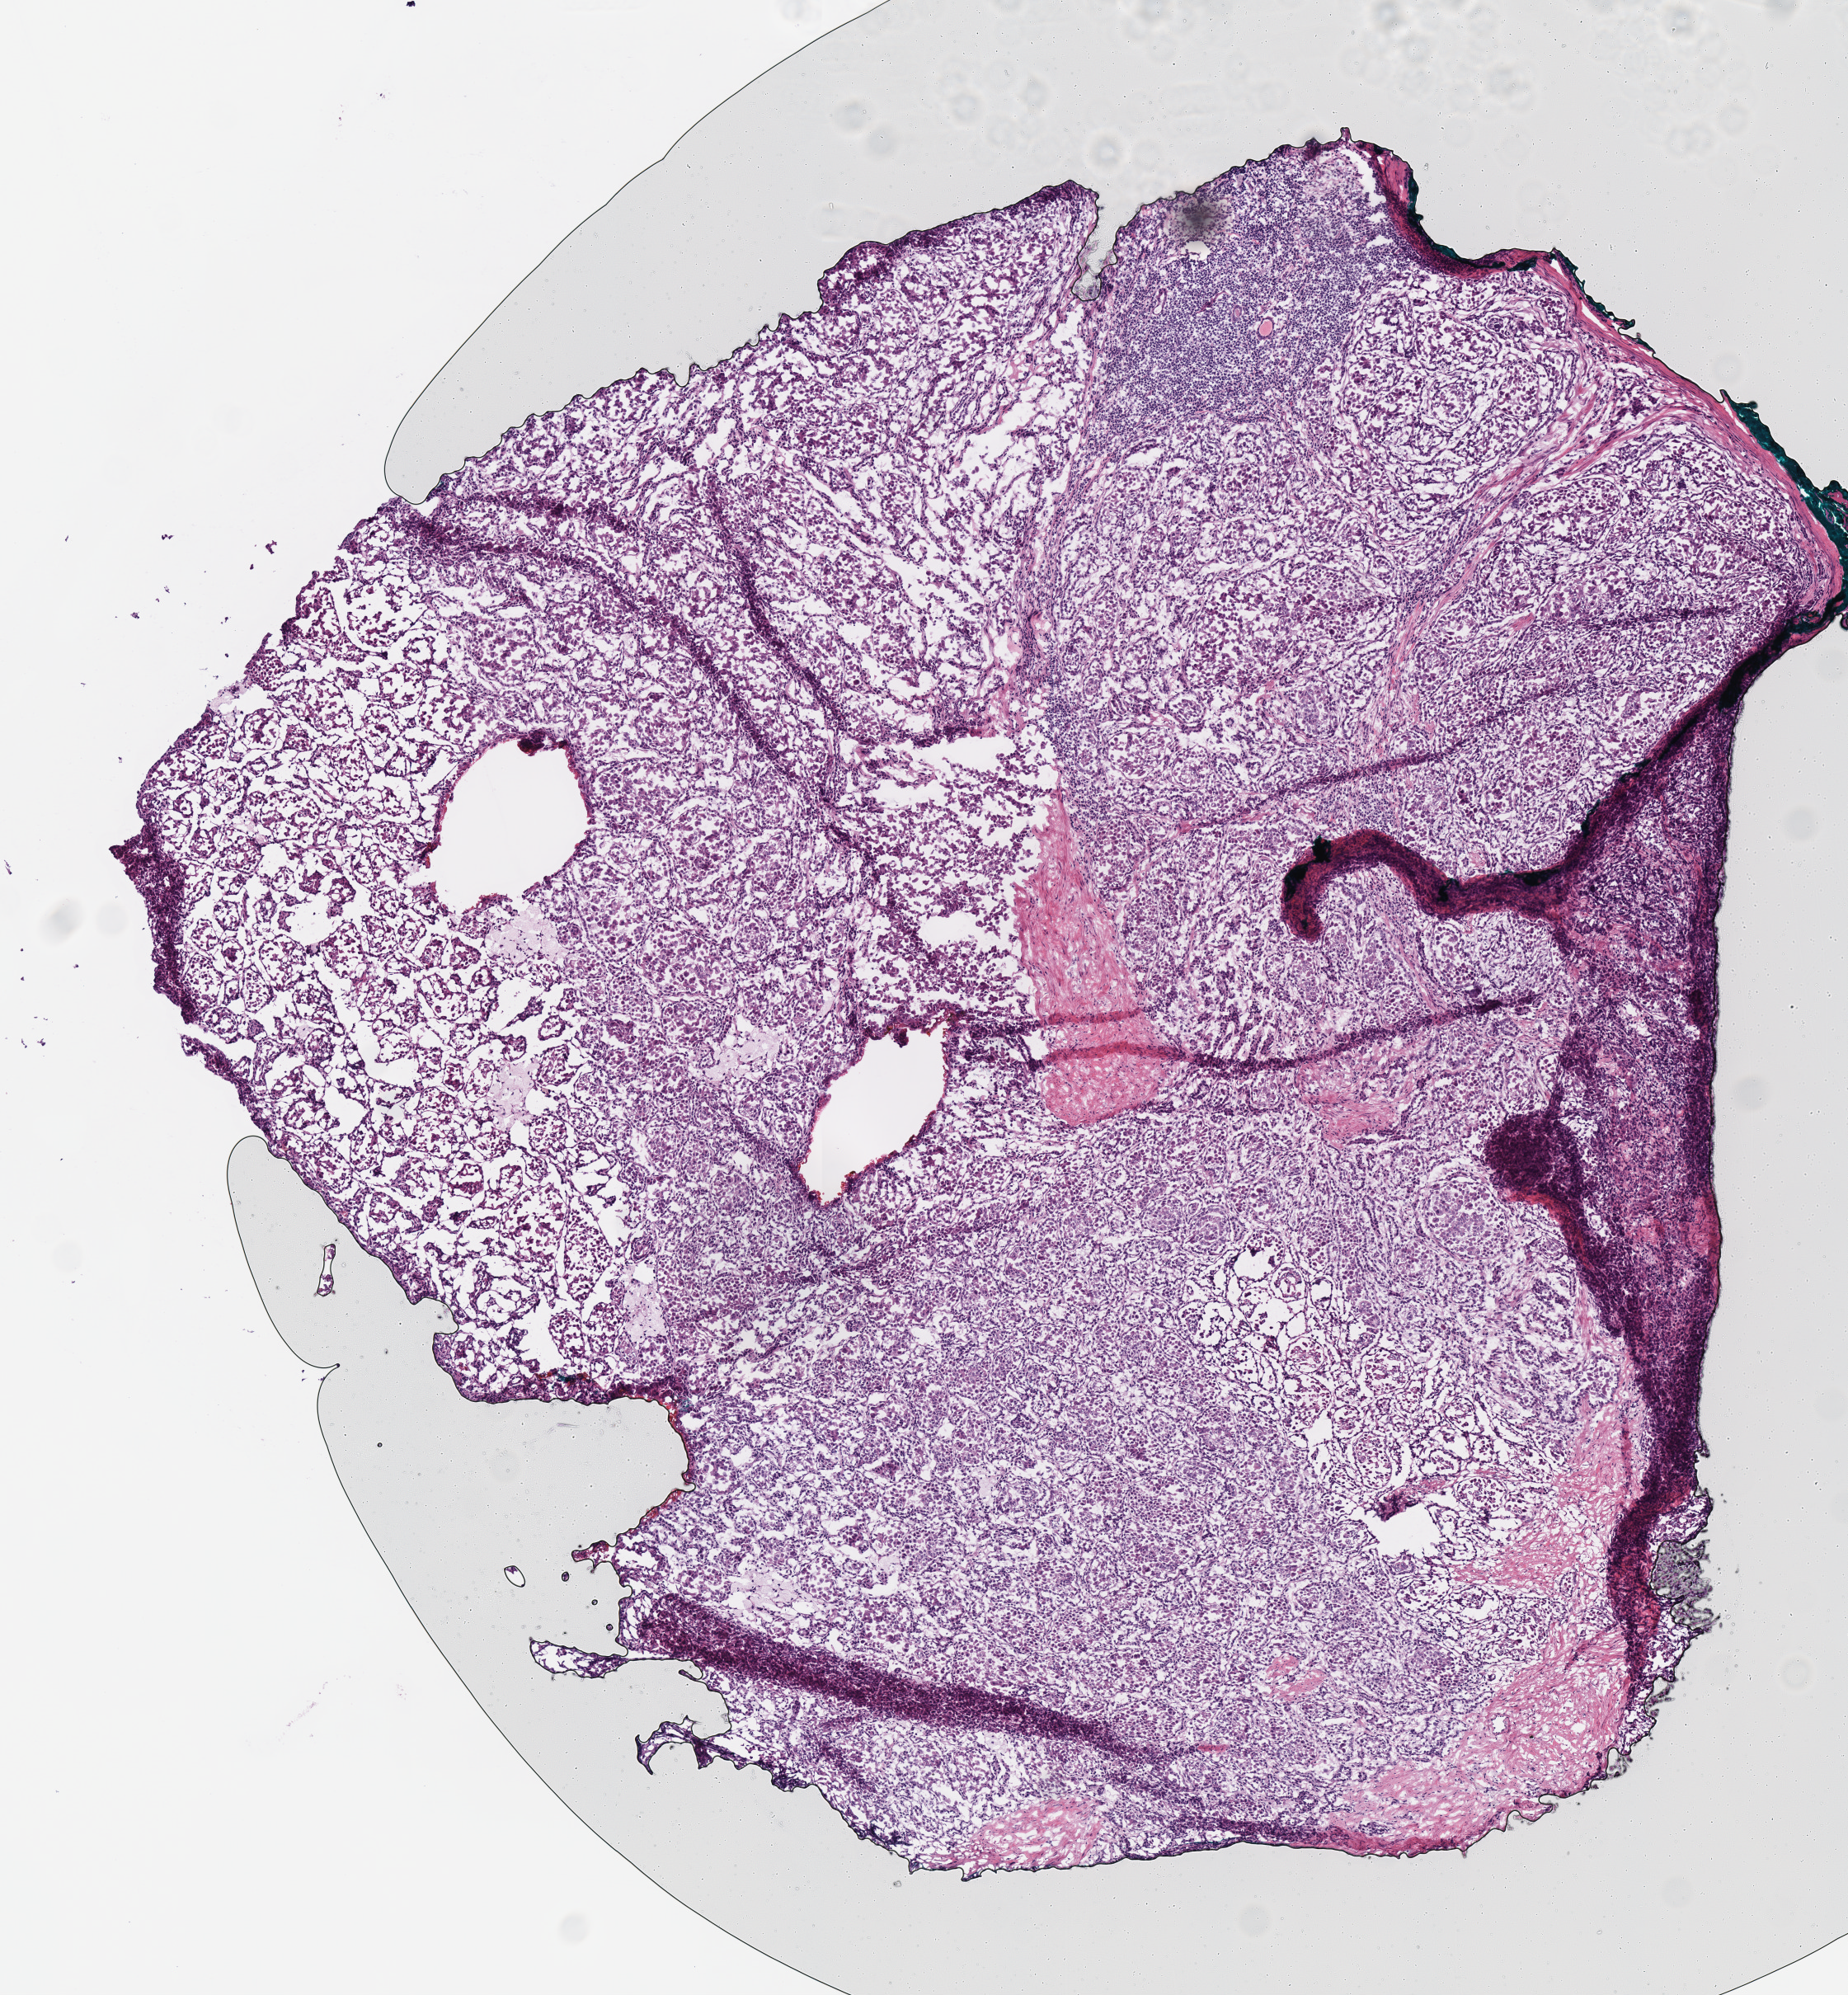
Whole-slide histology image, H&E-stained — a low-resolution overview of the entire scanned area, about 4.4 x 4.8 mm (slide scanned at 40x). Frozen section from the top of the tissue portion. Sample: primary tumour, kidney. Female patient; age at initial diagnosis 53 years. Pathologist review of this section (percent, as recorded): tumour nuclei 80%, necrosis 0%.
AJCC pathologic stage: I (7th edition). Diagnosis: Papillary adenocarcinoma, NOS.